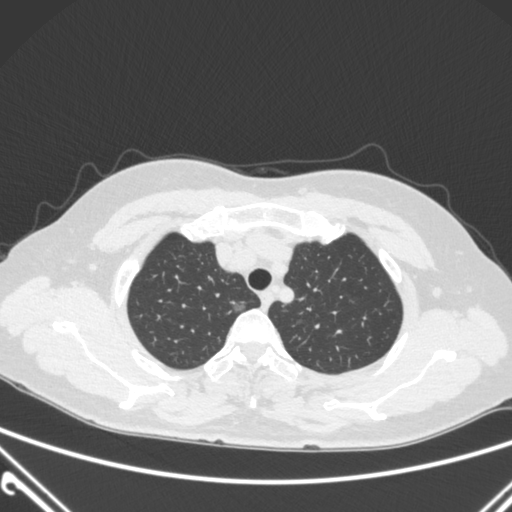
Chest CT, one axial slice; position 235 of 300 along the scan axis; 120 kVp; lung window (W 1500 / L -600 HU); 512 × 512 image matrix. Female patient, age 54 years. From the clinical record (not read from this slice): clinical TNM (as recorded): T1a N0 M0; histopathological grade: G1.
Outlined on this slice (rectangle marked by the reading radiologist):
- lung tumour (recorded histology: adenocarcinoma): box from (x=225, y=294) to (x=249, y=318) px